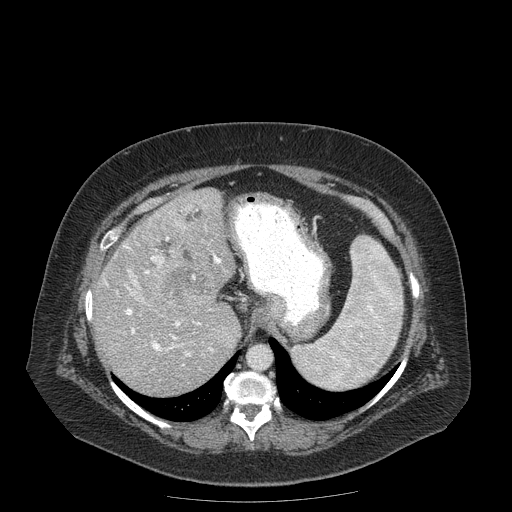
Contrast-enhanced abdominal CT (liver protocol), one axial slice; slice 131 of 204 in the series (ordered by position); reconstruction kernel STANDARD; 120 kVp; soft-tissue window (W 400 / L 40 HU); 512 × 512 image matrix. From the clinical record (not read from this slice): diagnosis: hepatocellular carcinoma (patient treated with transarterial chemoembolisation; whether this scan precedes or follows treatment is not stated here); TNM stage (as recorded): Stage-IIIB; Child-Pugh class: A; tumour differentiation: well differentiated; tumour nodularity: uninodular.
Structures marked on this image (semi-automatic segmentation, software-assisted and operator-edited):
- abdominal aorta: bounding box (x1, y1, x2, y2) in pixels: (247, 346, 270, 368)
- liver parenchyma outside the tumour (the mass and vessels are separate outlines, so this box may not span the whole liver): (93, 188, 240, 394)
- mass: (146, 256, 217, 316)
- liver vessels: (105, 208, 221, 356)